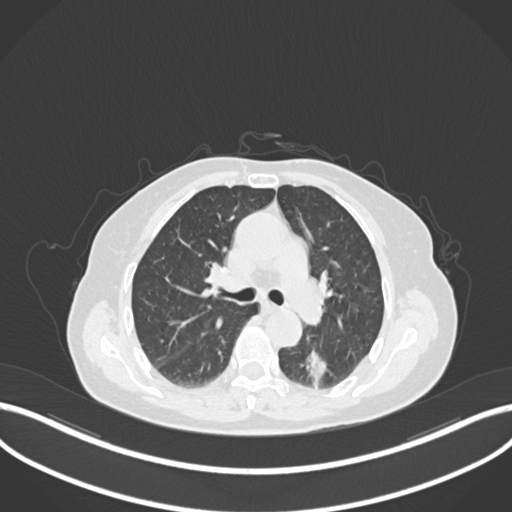
Chest CT, one axial slice. Slice 532 of 727 in the series (ordered by position). 120 kVp. Lung window (W 1500 / L -600 HU). 1 mm slice thickness. 512 × 512 image matrix, field of view 400 × 400 mm. Female patient, age 70 years. From the clinical record (not read from this slice): clinical TNM (as recorded): T1c N0 M0.
Annotated regions visible in this slice (bounding box drawn by a radiologist):
- lung tumour (recorded histology: adenocarcinoma): bounding box [x1, y1, x2, y2] px = [303, 350, 333, 384]